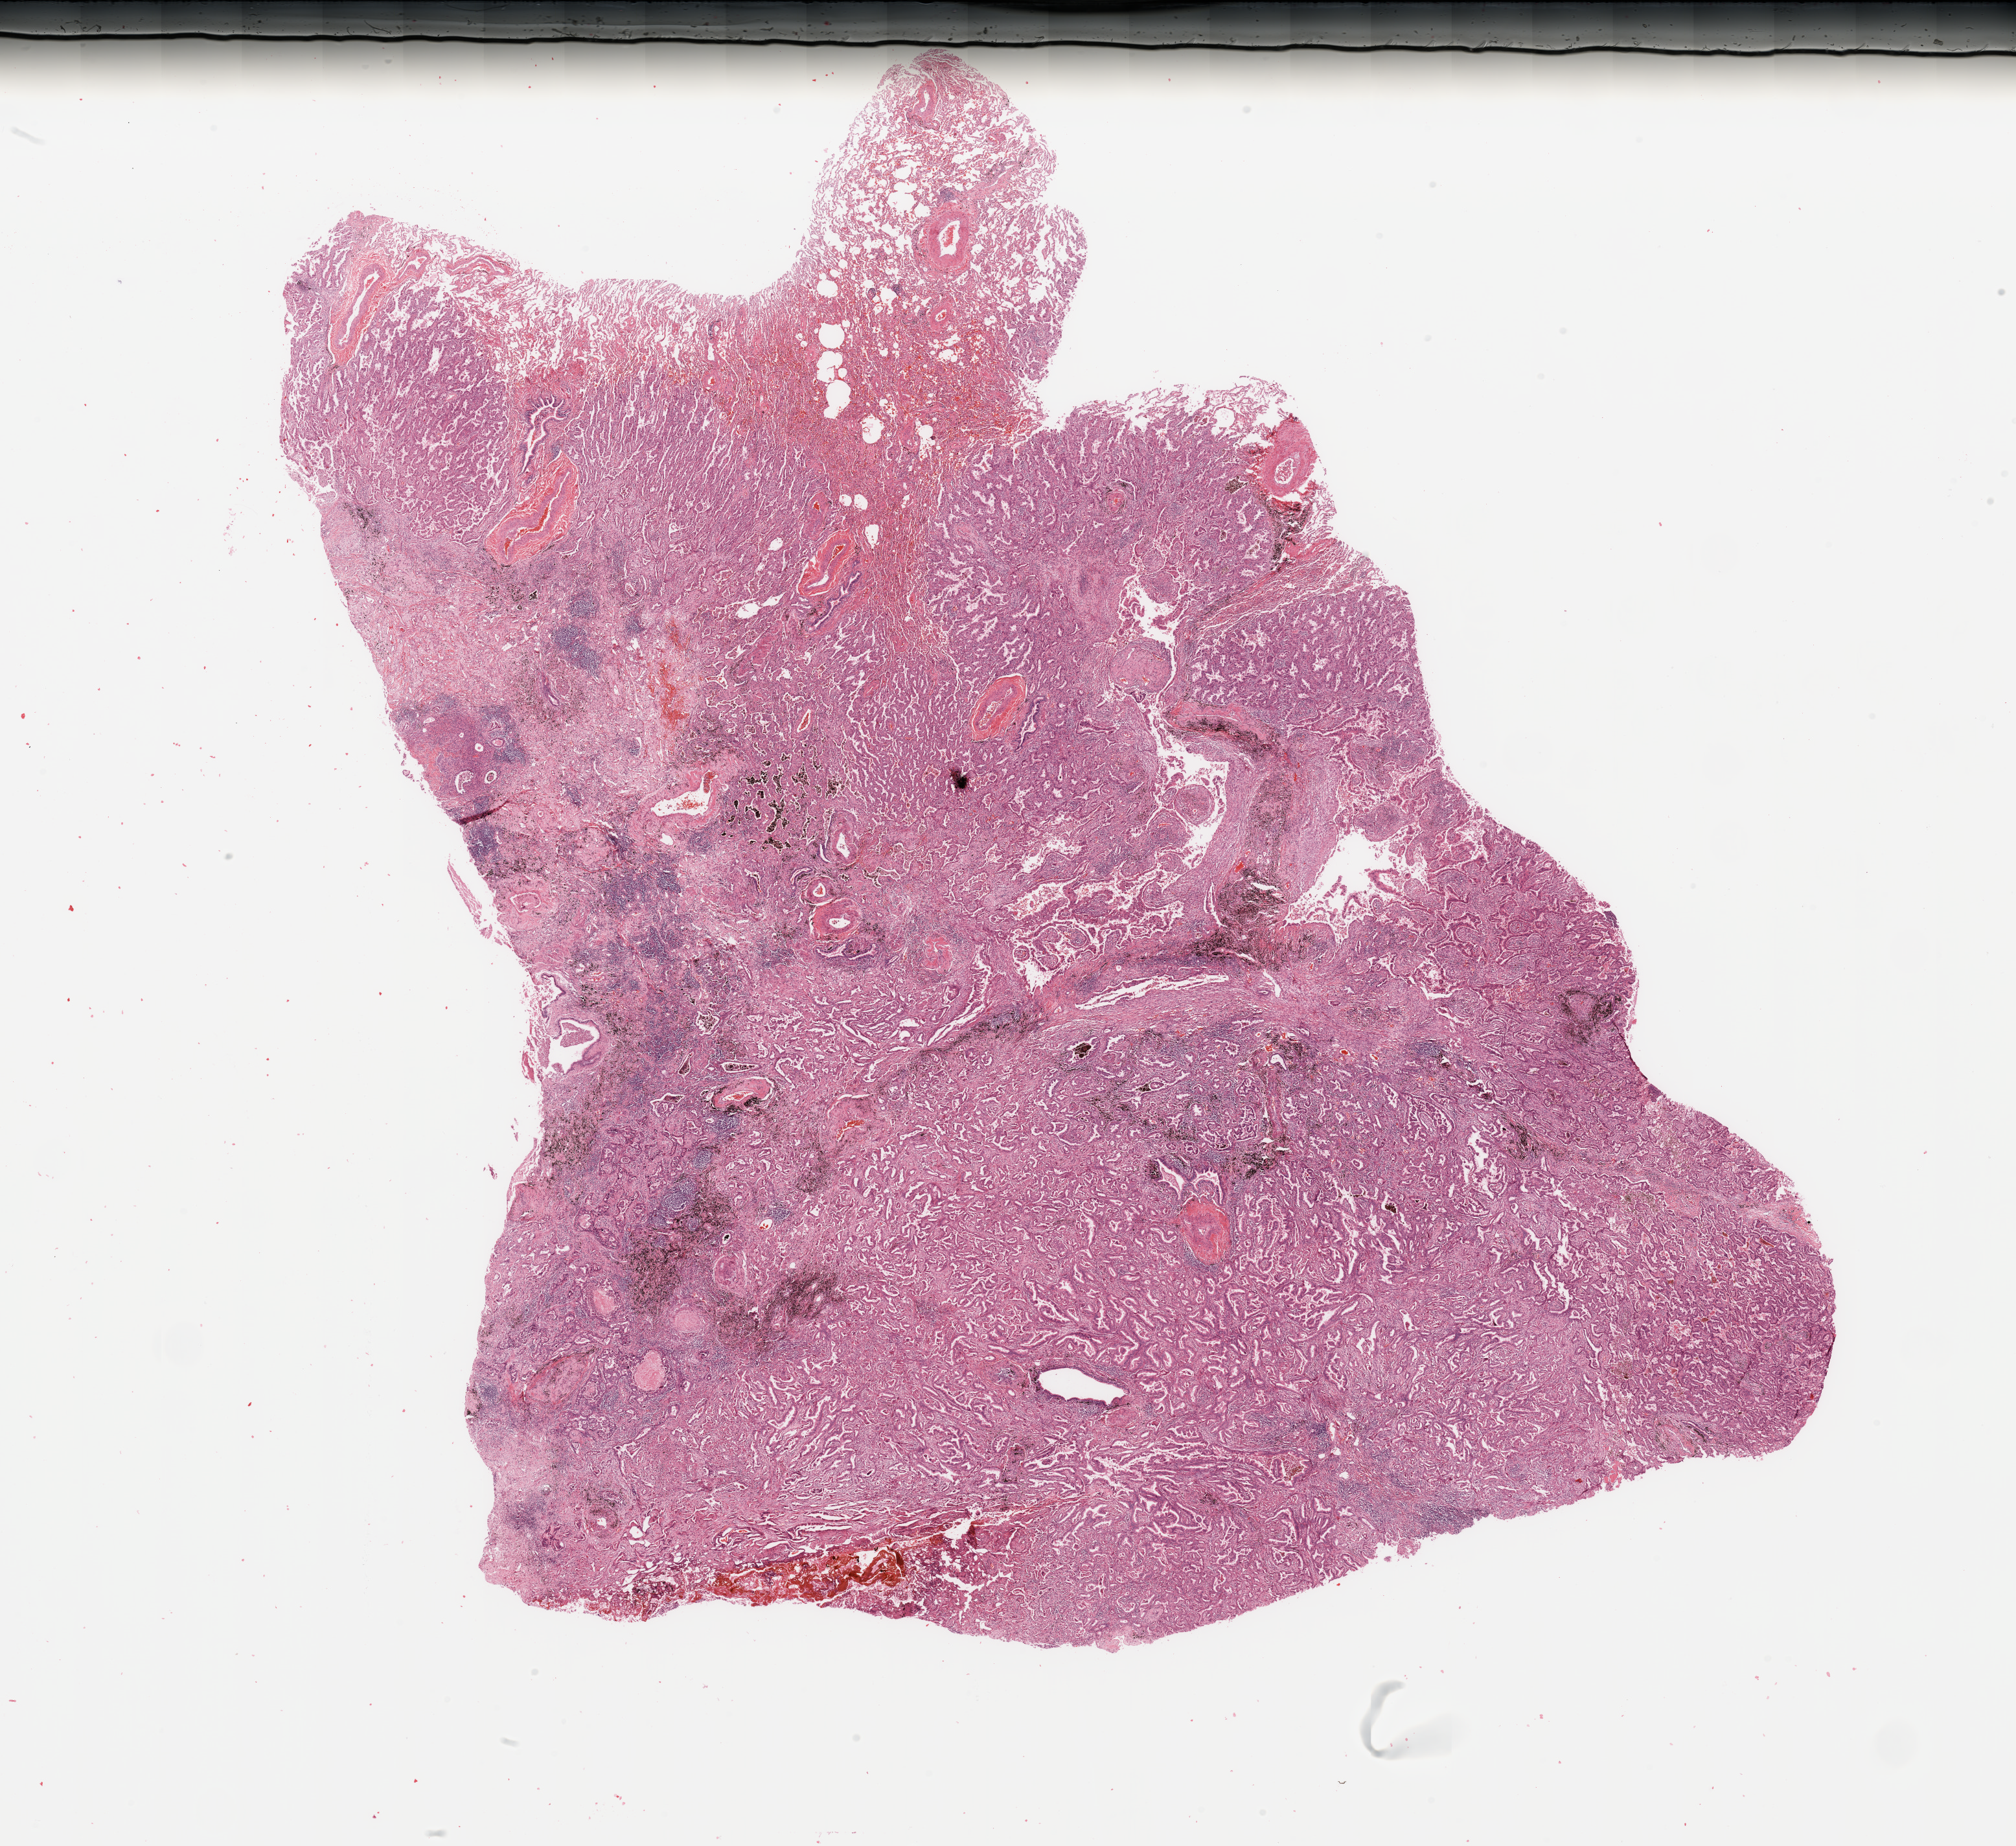
Hematoxylin and eosin (H&E) stained whole-slide image, low-resolution overview of the scanned area, about 24.6 x 22.5 mm (slide scanned at 20x); tumour tissue sample, lung. Female, 68 y/o. Histologic grade: G2 (moderately differentiated).
AJCC pathologic stage: IB. Histologic diagnosis: Adenocarcinoma, NOS.